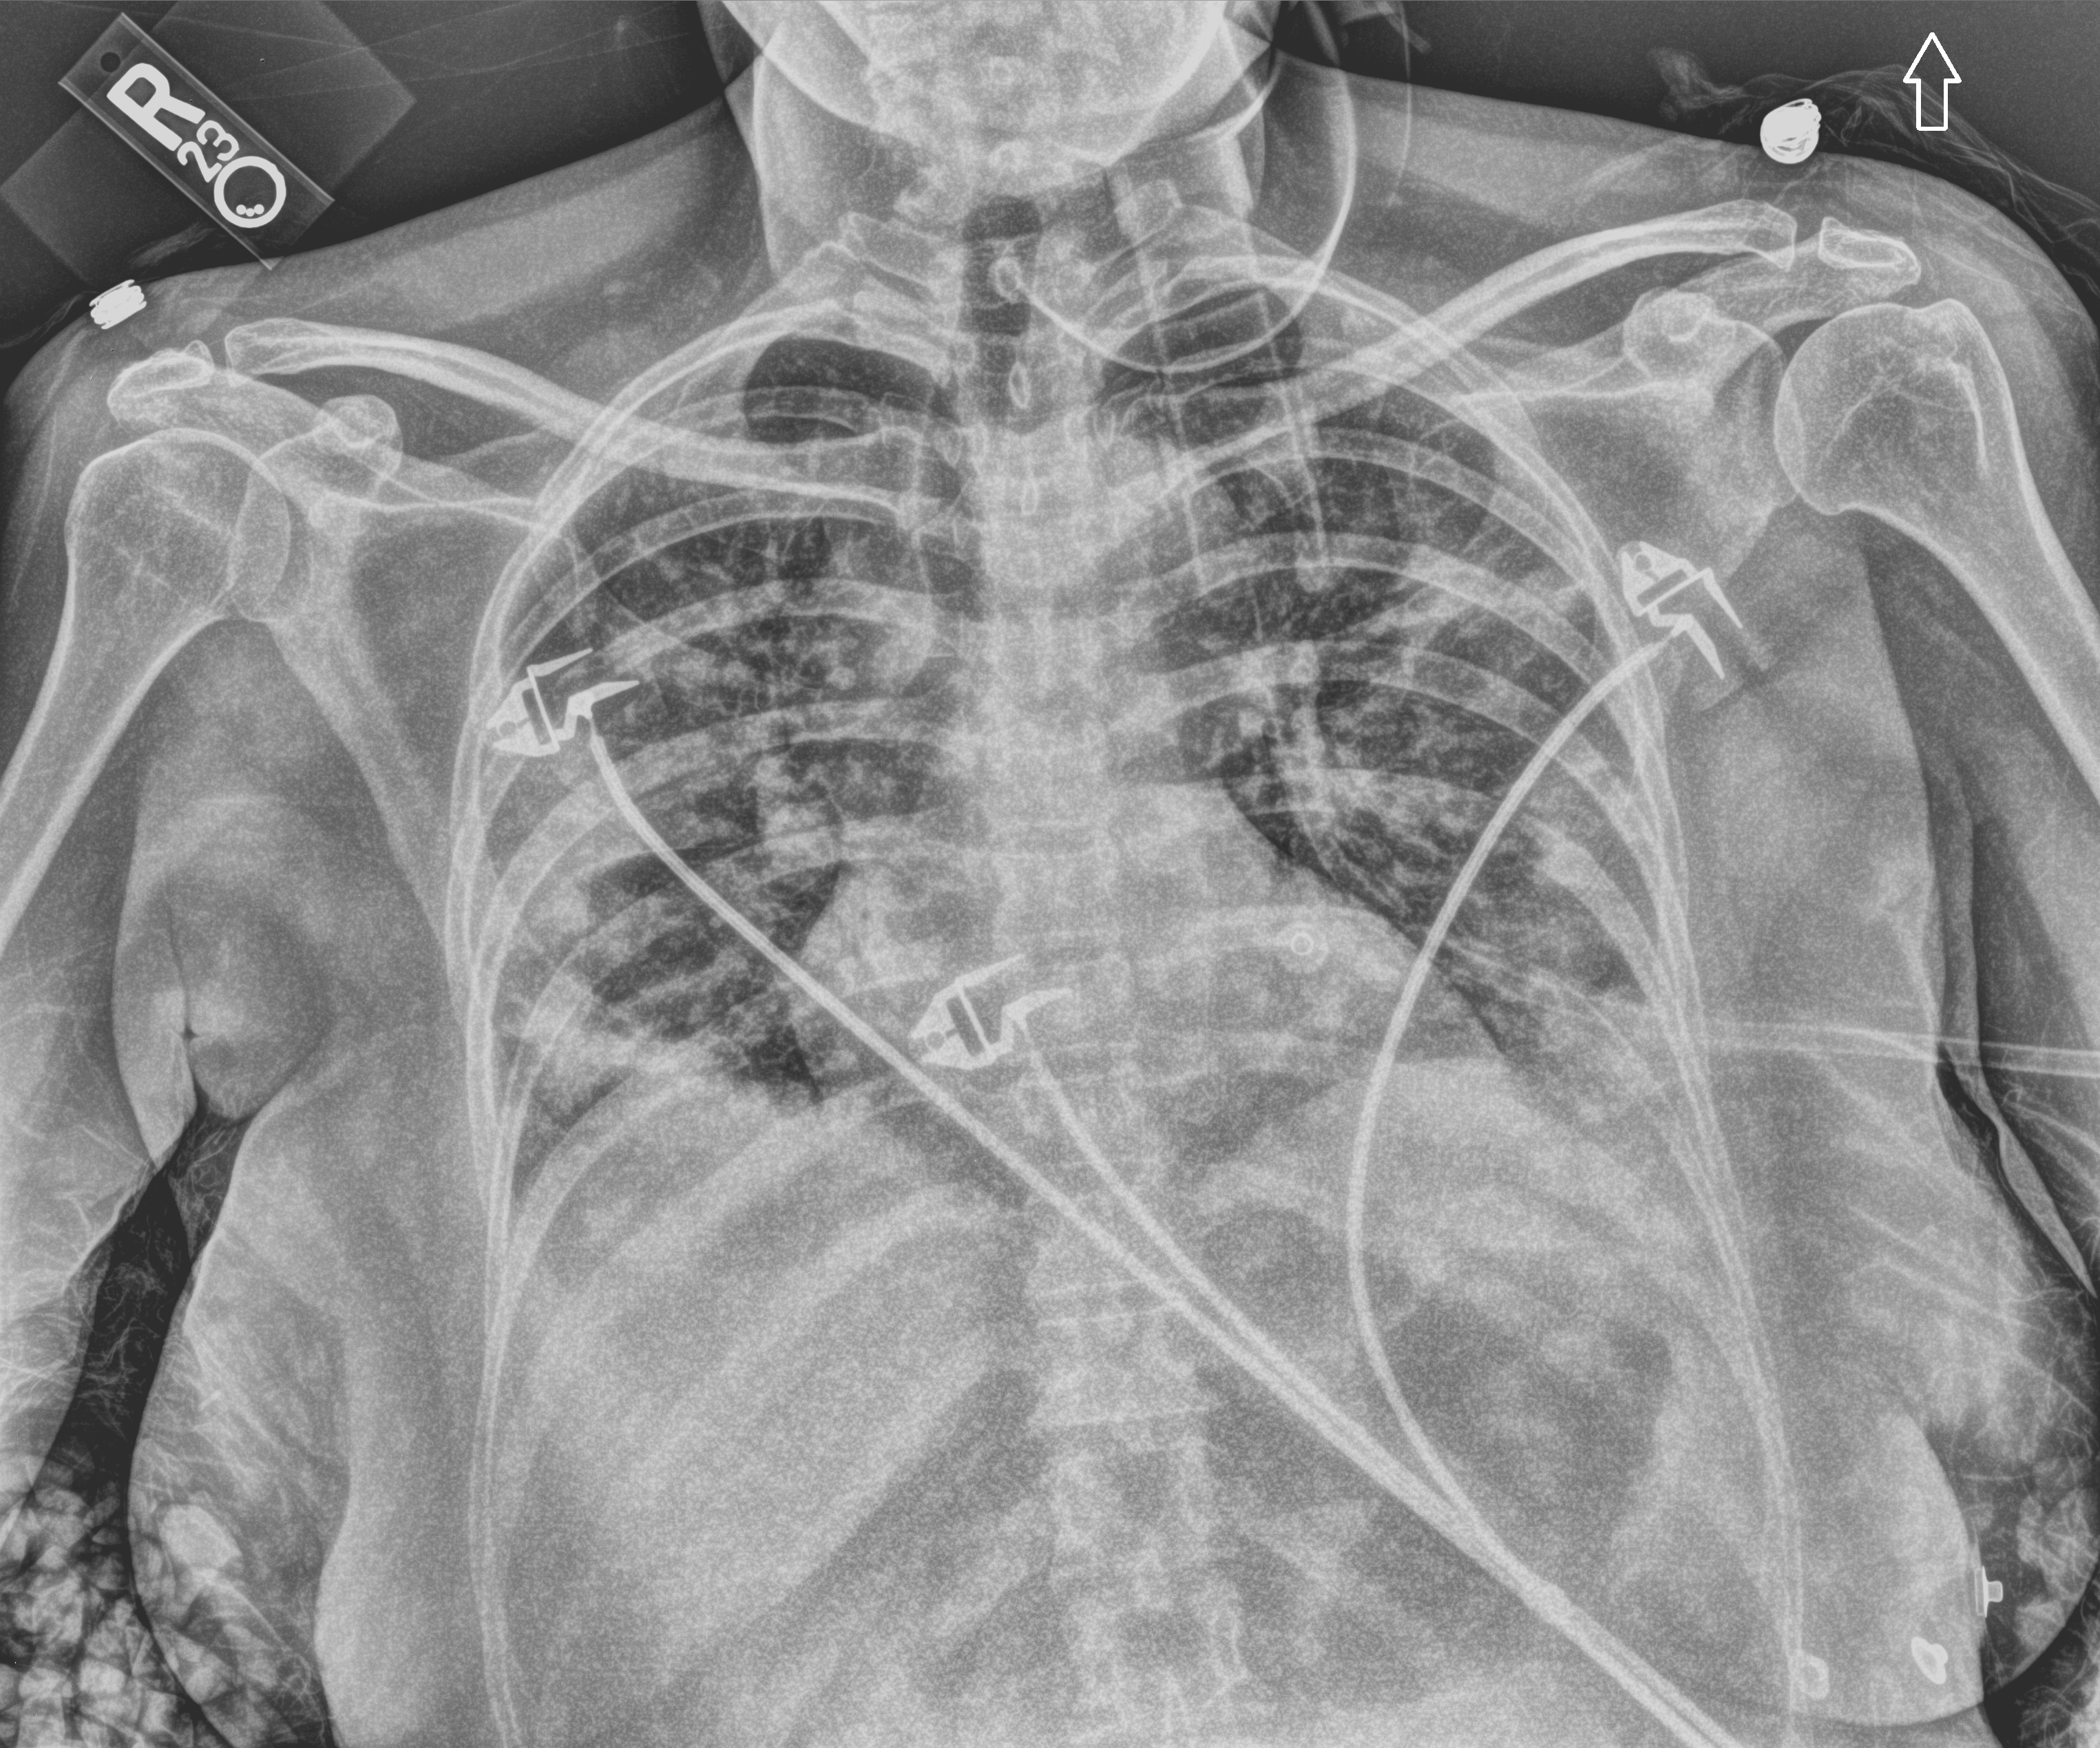
Bedside chest radiograph (computed radiography), anteroposterior (AP) projection. Patient hospitalised with COVID-19; female, aged 18–59 years.
Hospital-stay facts (about this admission, not read from this image; timing relative to this image not recorded):
- mechanically ventilated during this hospital stay: yes